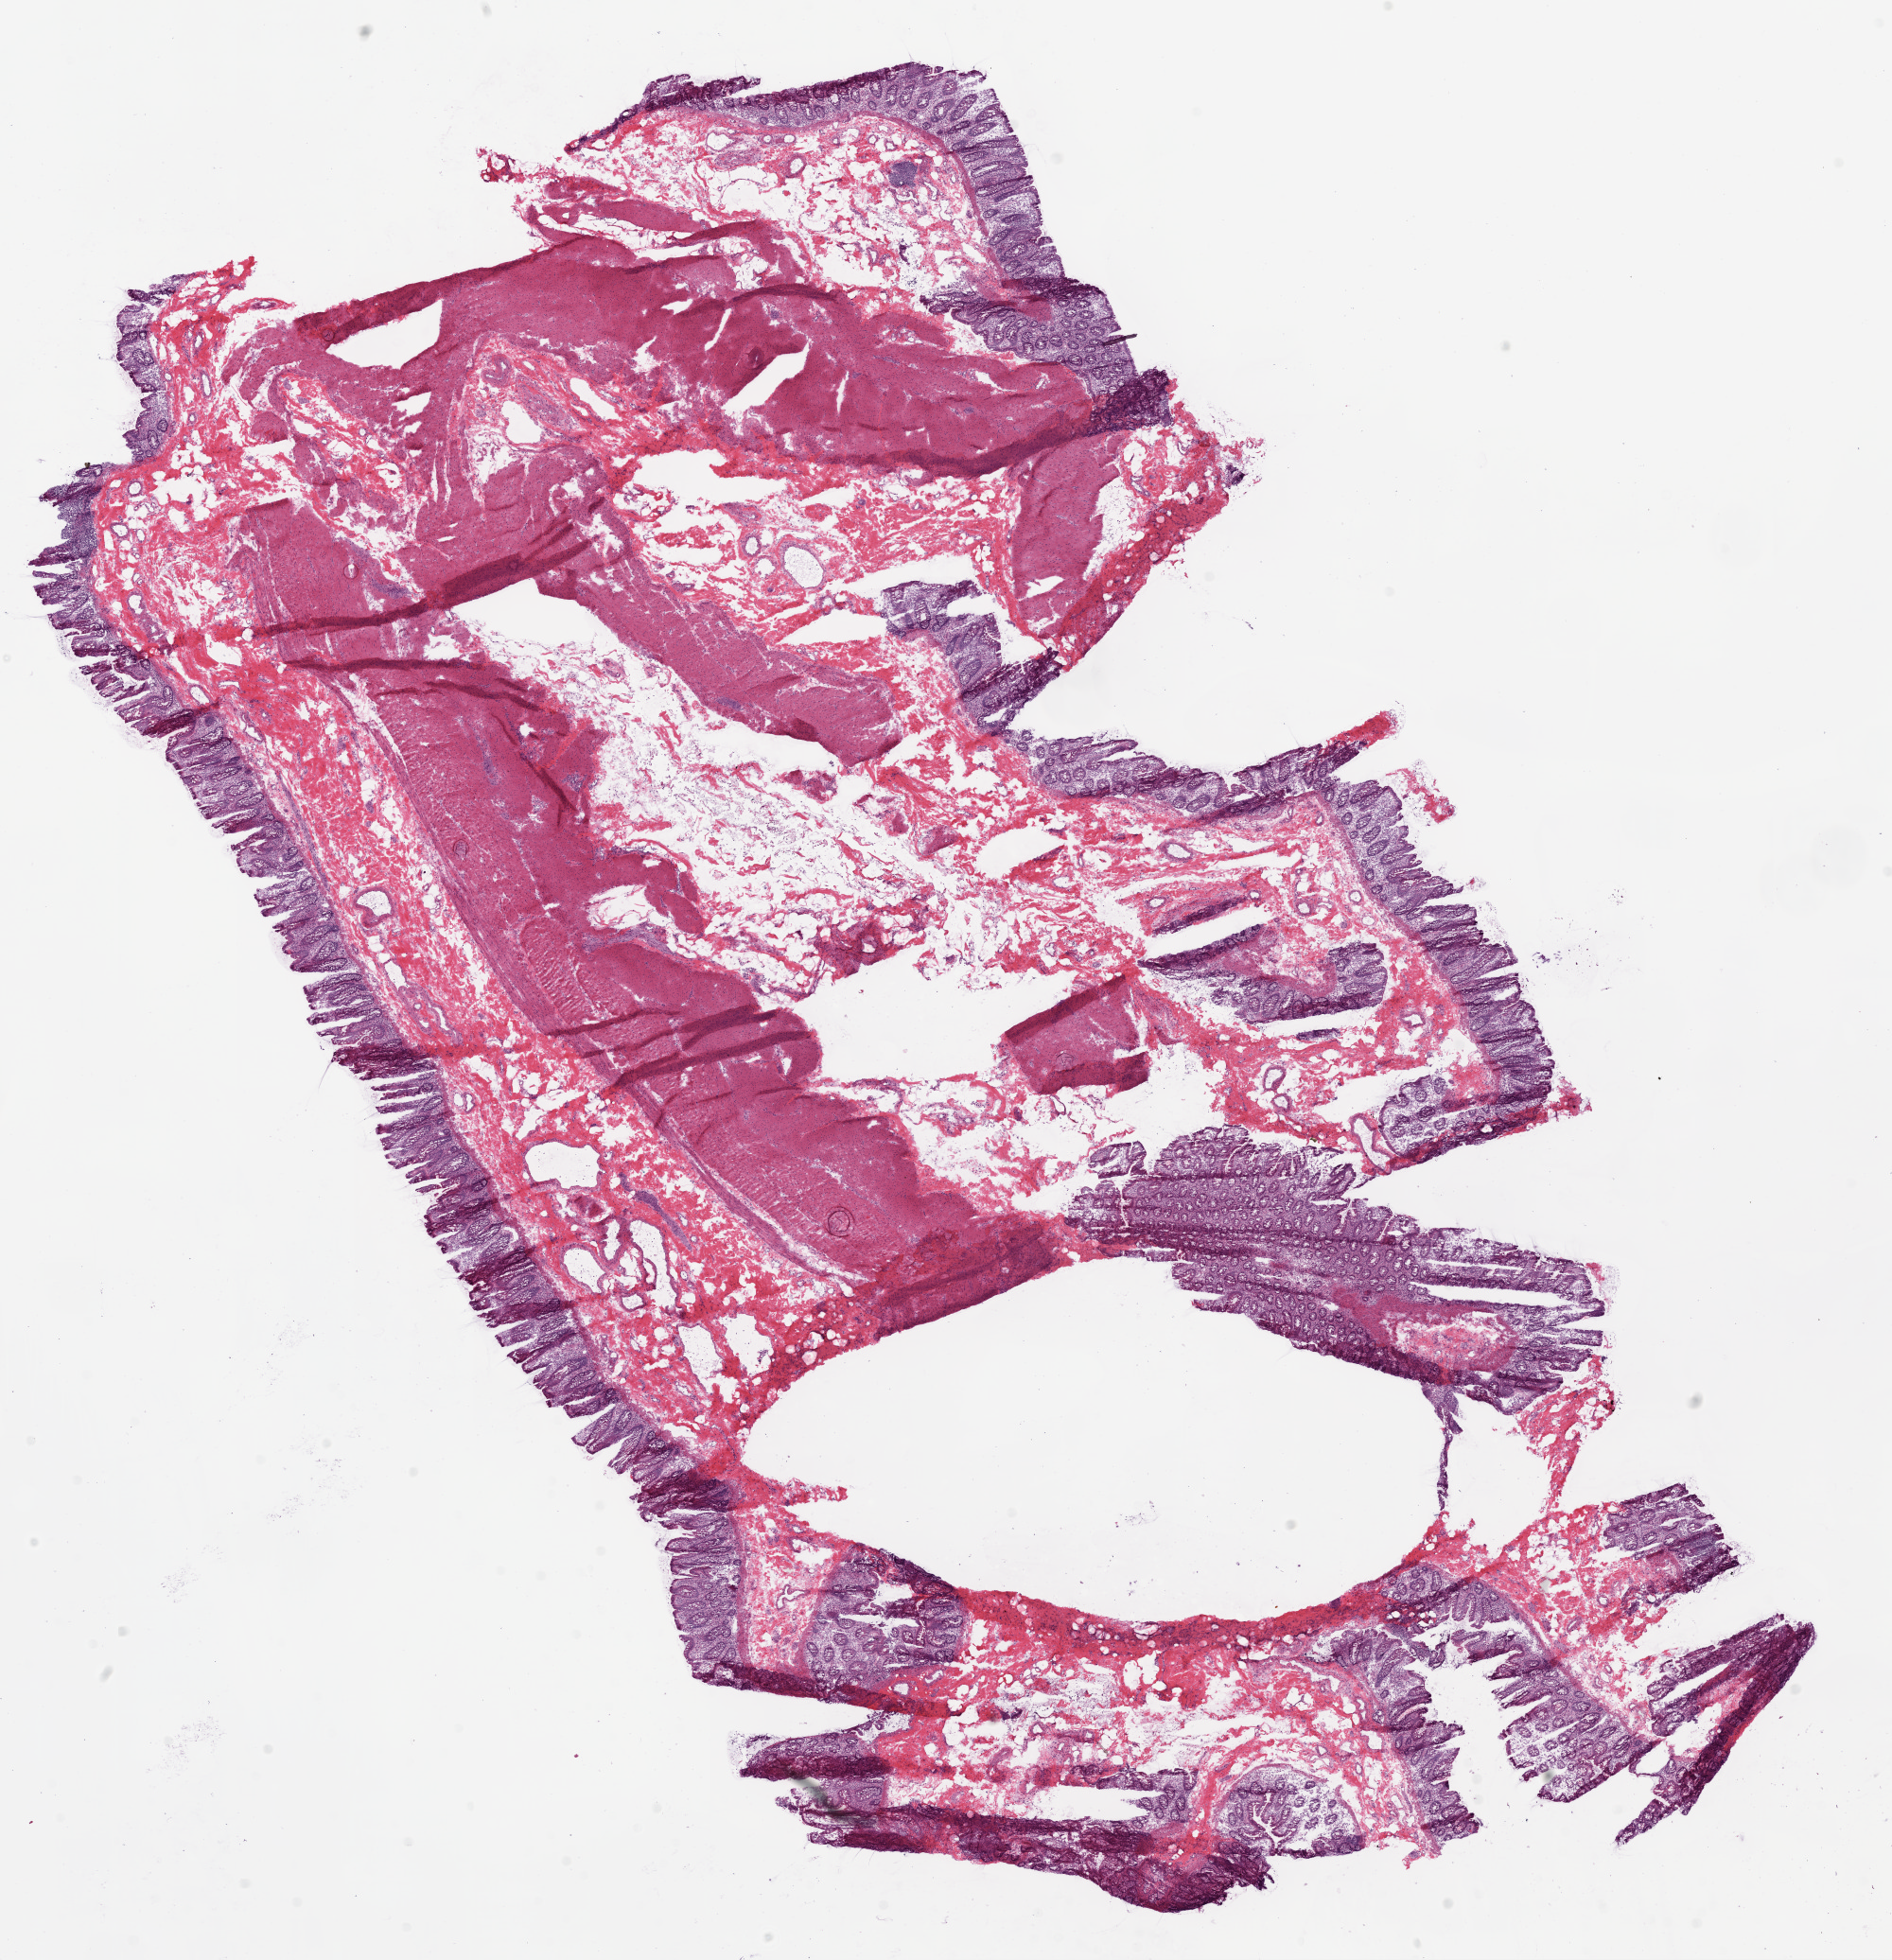
H&E-stained whole-slide image, whole scanned area (about 16.0 x 16.6 mm) shown as a low-resolution overview, frozen section from the bottom of the tissue portion, solid tissue normal (non-tumour tissue) sample from the colon. Patient: female, age at initial diagnosis 57 years.
This section: solid tissue normal sample (biorepository sample class). Patient diagnosis: Adenocarcinoma, NOS (ascending colon).